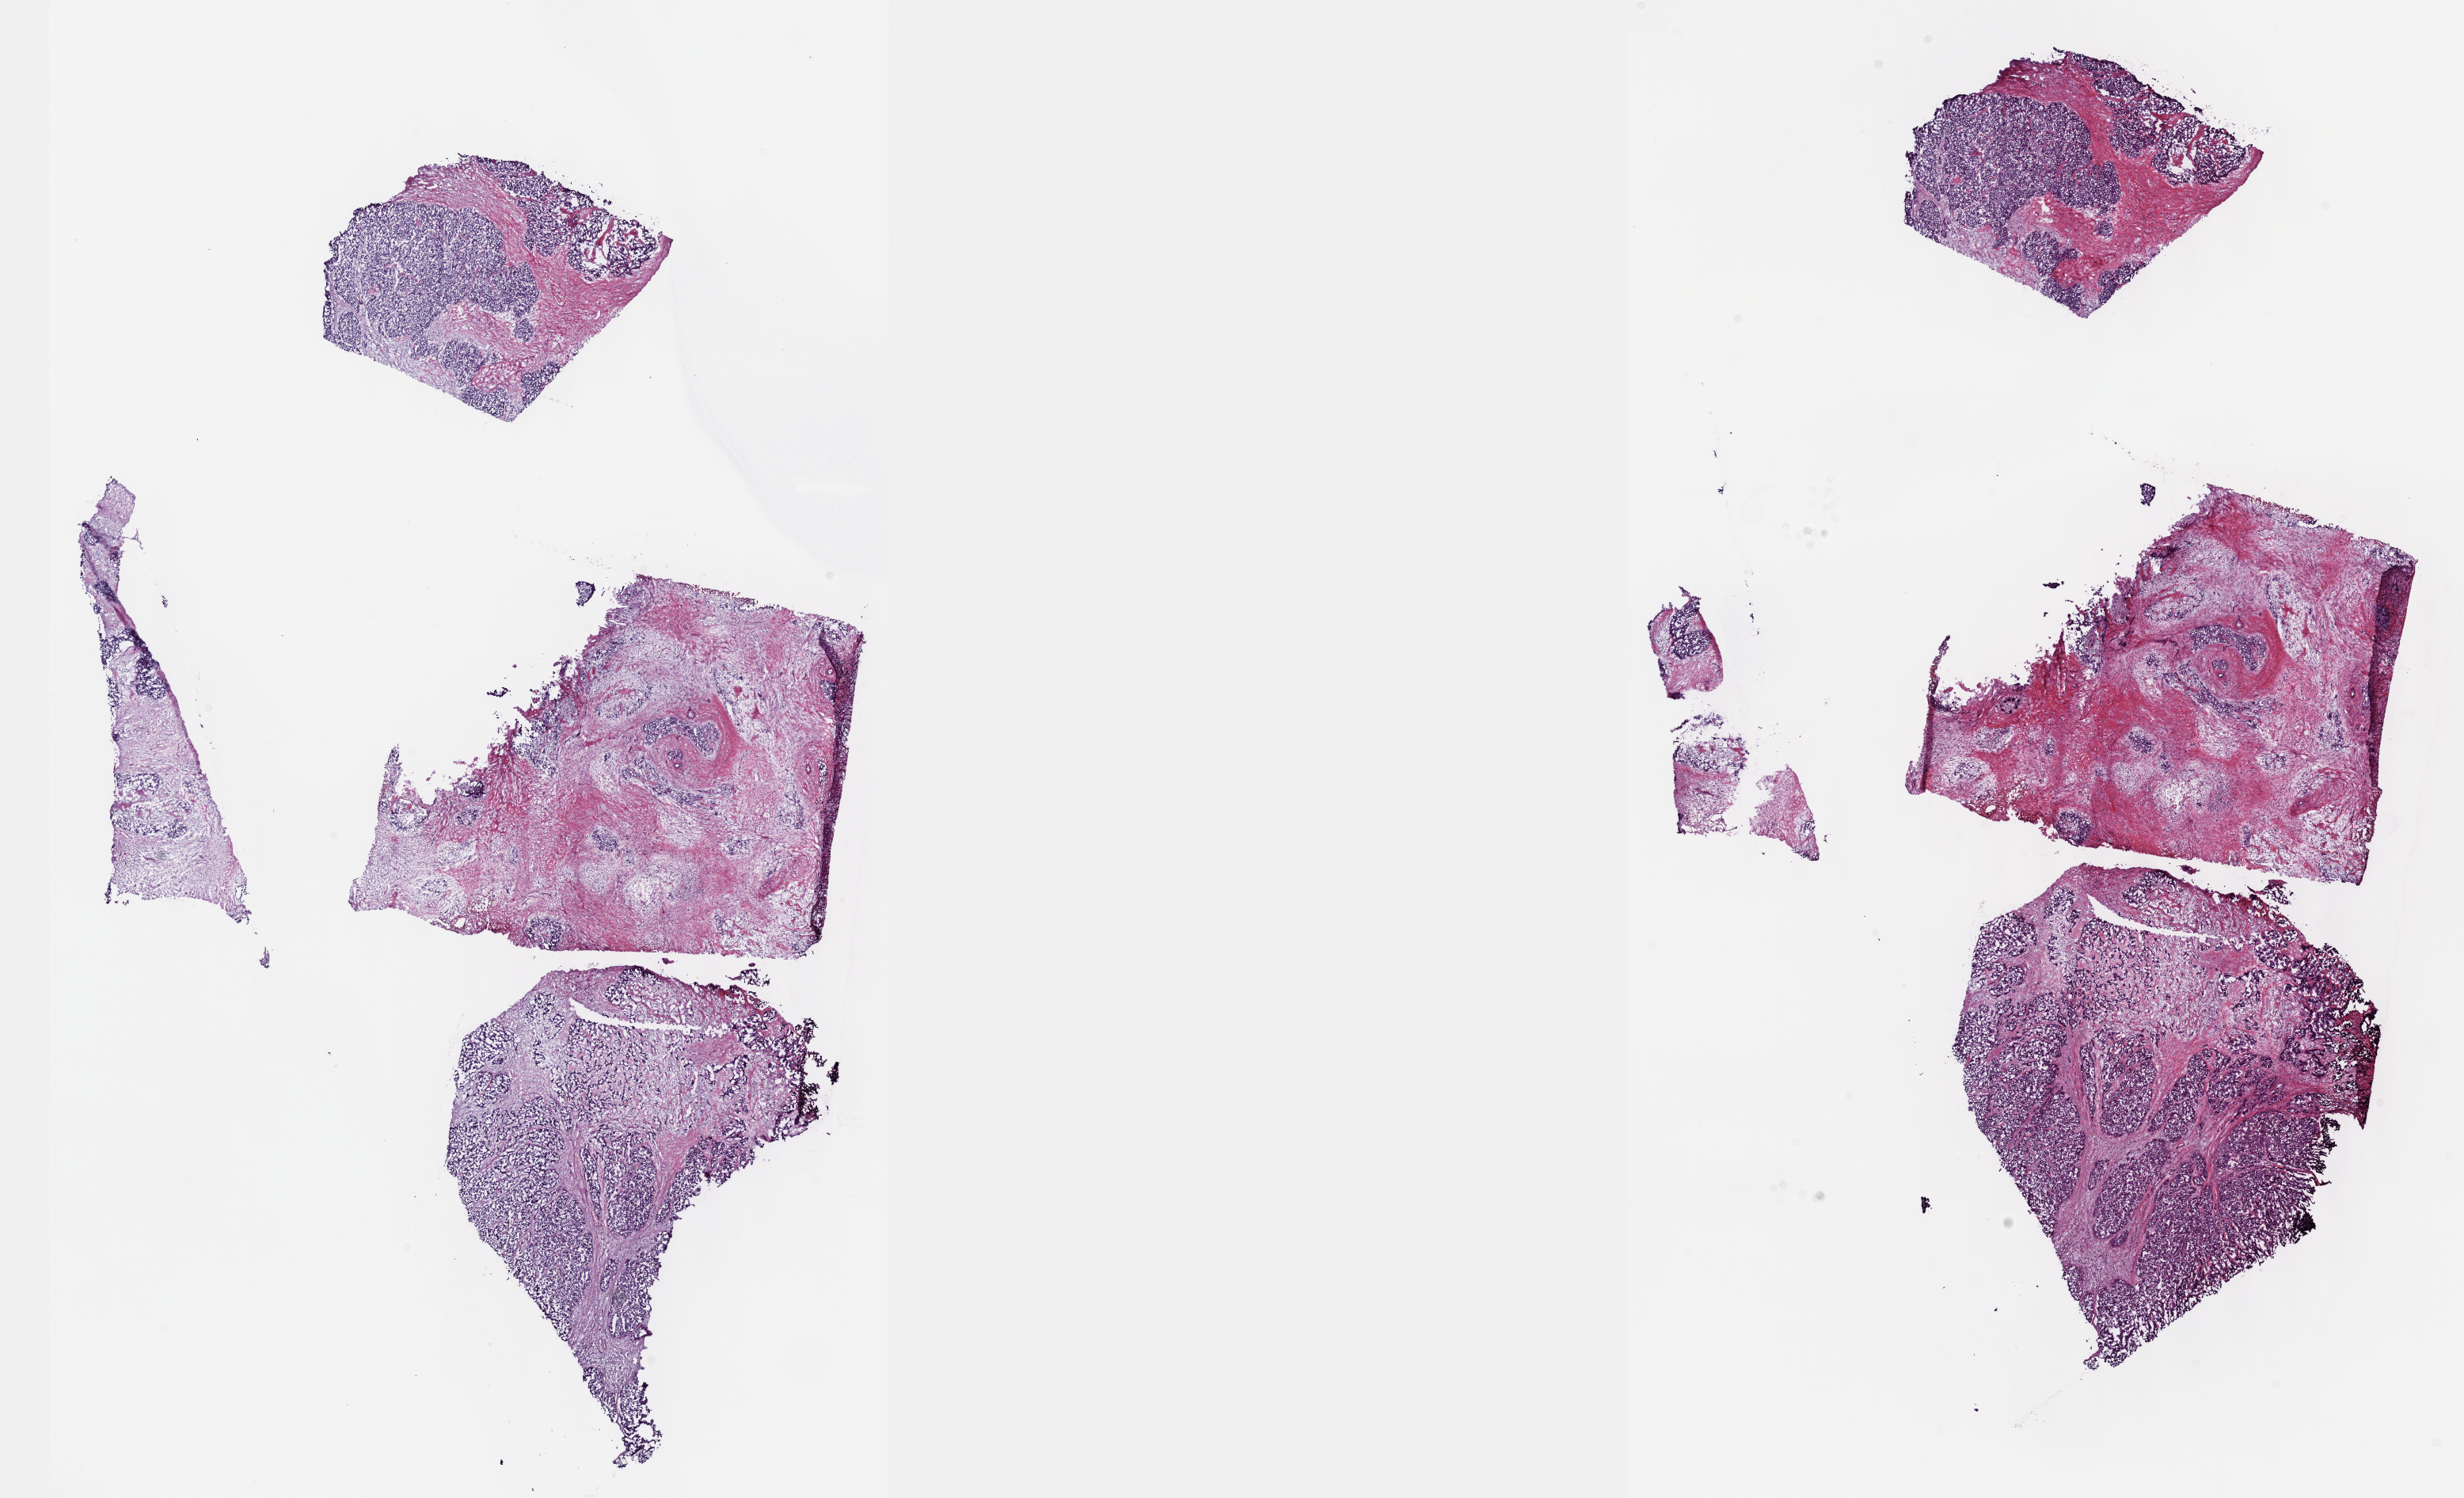
Digitized H&E tissue section (whole slide) — low-resolution overview of the scanned area, about 25.1 x 15.3 mm (from a 40x scan). Frozen section from the top of the tissue portion. Primary tumour sample from the liver. Female, age 64 years at initial diagnosis. Histologic grade: G3 (poorly differentiated). Pathologist review of this section (percent, as recorded): tumour cells 70%, tumour nuclei 70%, normal cells 0%, stromal cells 30%, necrosis 0%. Infiltration values recorded for this section: lymphocyte infiltration 3%, monocyte infiltration 1%, neutrophil infiltration 4%.
Pathologic diagnosis: Hepatocellular carcinoma, NOS. AJCC pathologic stage: I.